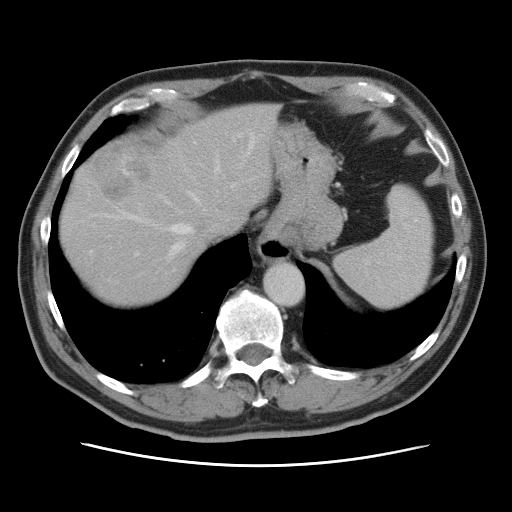
Contrast-enhanced abdominal CT, one axial slice; position 64 of 80 along the scan axis; intravenous contrast given; soft-tissue window (W 400 / L 40 HU); 5 mm slice thickness; 512 × 512 image matrix. Male patient, age 69 years. From the clinical record (not read from this slice): diagnosis: colorectal cancer liver metastases, imaged before liver resection.
Structures marked on this image (outlined manually by an expert reader):
- hepatic veins: bounding box (x1, y1, x2, y2) in pixels: (90, 131, 256, 257)
- liver: (61, 104, 278, 304)
- planned liver remnant (the part of the liver to remain after resection): (60, 103, 277, 305)
- portal vein (with intrahepatic branches): (135, 134, 234, 256)
- liver metastasis: (92, 150, 151, 202)